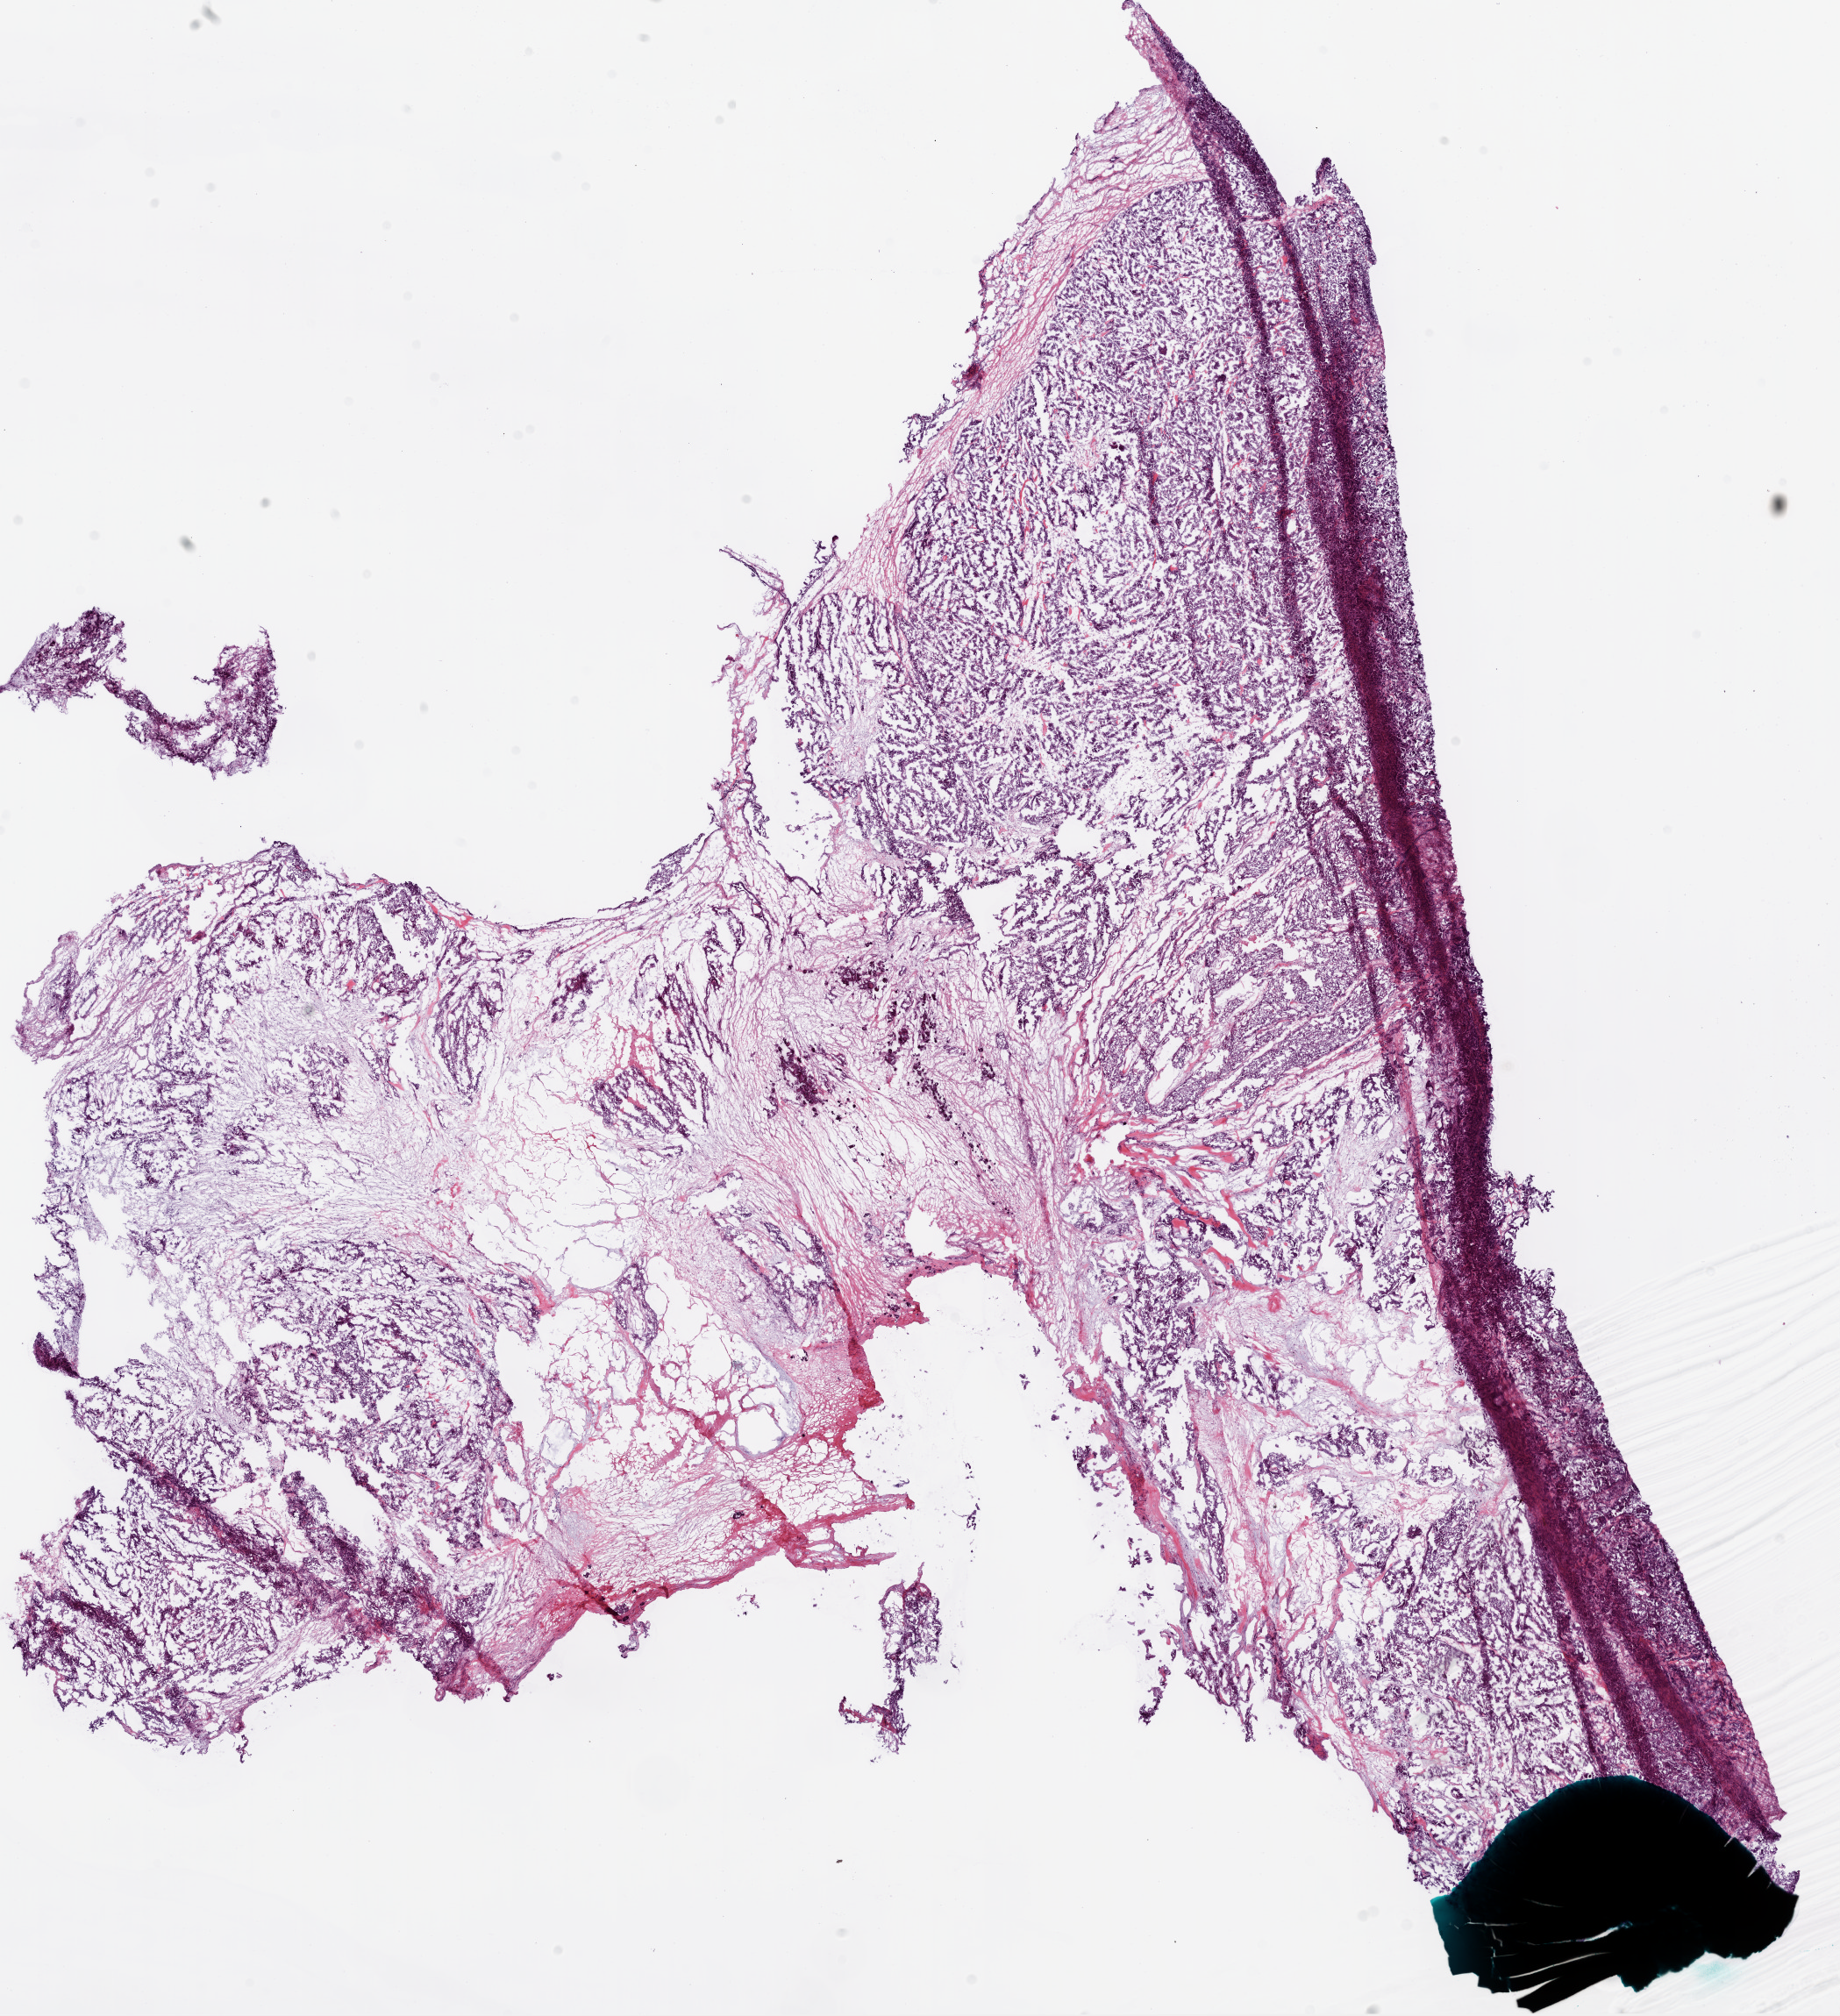
Whole-slide histology image, H&E, low-resolution overview of the scanned area, about 16.9 x 18.5 mm (acquisition: 20x scan). Frozen section from the bottom of the tissue portion. Ovary, primary tumour sample. Patient: female, age at initial diagnosis 54 years. Histologic grade: G3 (poorly differentiated). Pathologist review of this section (percent, as recorded): tumour cells 85%, tumour nuclei 95%, stromal cells 10%, necrosis 5%.
- FIGO stage: IIIC
- diagnosis: Serous cystadenocarcinoma, NOS